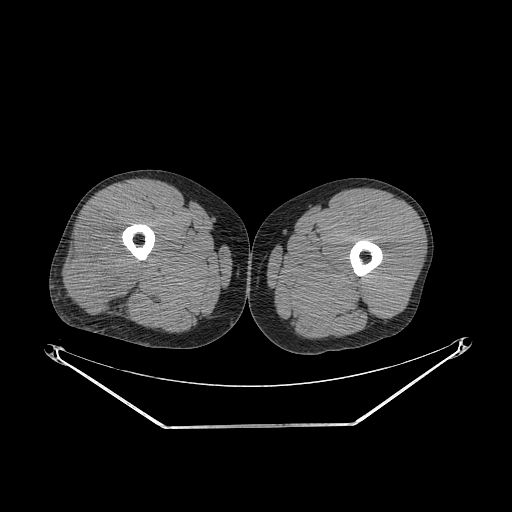
CT of an extremity soft-tissue mass (from a PET/CT study), one axial slice. Position 246 of 267 along the scan axis. Soft-tissue window (W 400 / L 40 HU). 3.75 mm slice thickness. 512 × 512 image matrix, field of view 500 × 500 mm. Male patient. From the clinical record (not read from this slice): histological type: poorly differentiated synovial sarcoma; grade: high; site of the primary tumour: right buttock.
Outlined on this slice (expert contour drawn on MRI and transferred to this co-registered scan by the dataset authors):
- gross tumour volume including surrounding oedema: bounding box <66,219,140,312> (left, top, right, bottom; pixels)
- gross tumour volume (mass): <69,219,138,309>